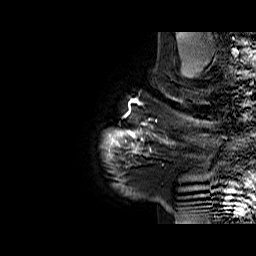
Breast MRI (dynamic contrast-enhanced), one sagittal slice. Dynamic contrast-enhanced series, time point 2 of 6 at this slice position (early post-contrast). 1.5 T. TE 6.1 ms, TR 32.9 ms. 4 mm slice thickness. 256 × 256 image matrix. Female patient. Case-level facts recorded for this patient, not image findings: setting: breast cancer imaged before/during neoadjuvant chemotherapy; receptor status: HER2-positive.
Annotated regions visible in this slice (semi-automatic segmentation, software-assisted and operator-edited):
- analysis volume of interest (the breast-tissue region the enhancement analysis was run in; not a lesion): box from (x=127, y=95) to (x=194, y=165) px
- tumour enhancement mask (voxels above the 100 % enhancement threshold inside the analysis volume of interest): (x=127, y=96)–(x=194, y=156)